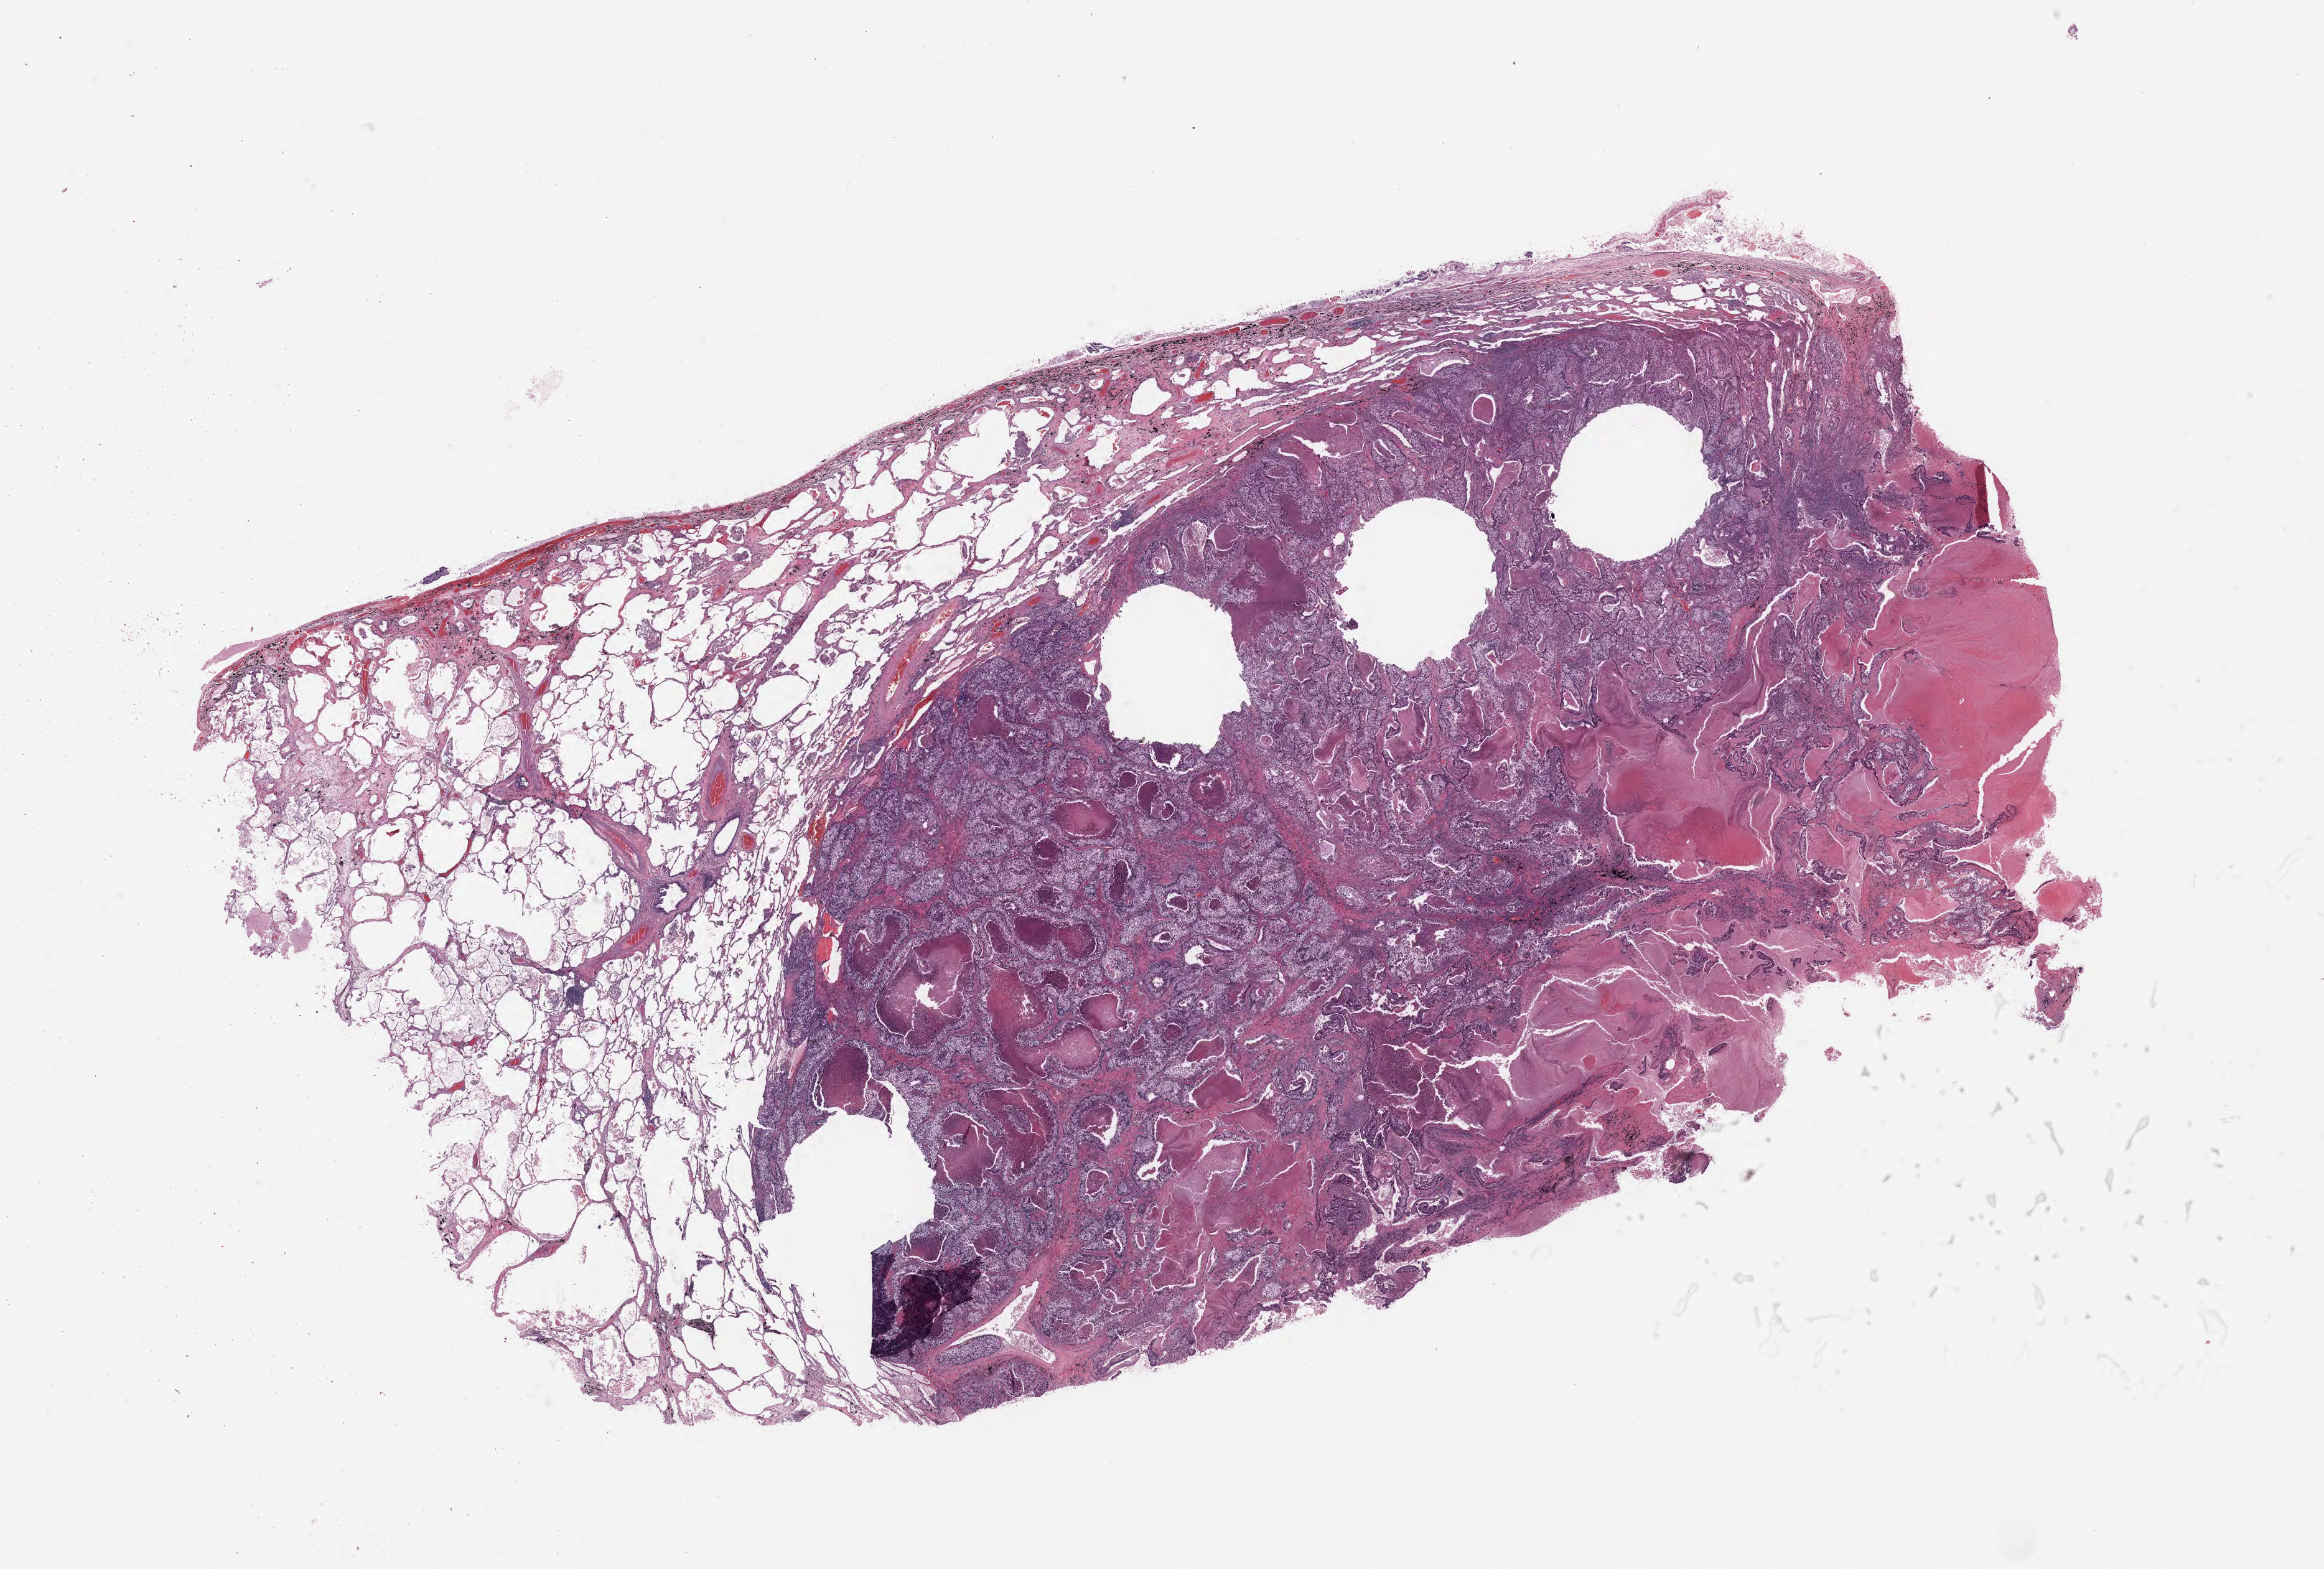
Digitized haematoxylin and eosin-stained section, a low-resolution overview of the entire scanned area, about 30.2 x 20.4 mm. Specimen: tumor tissue. Anatomic site: lung. Patient sex: female.
Histologic diagnosis: Adenocarcinoma, NOS.